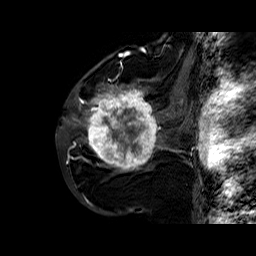
Breast MRI (dynamic contrast-enhanced), one sagittal slice; position 34 of 60 along the scan axis; dynamic contrast-enhanced series, time point 2 of 6 at this slice position (early post-contrast); 1.5 T; TE 6.4 ms, TR 32.8 ms; 256 × 256 image matrix, field of view 200 × 200 mm. Female patient. From the clinical record (not read from this slice): setting: breast cancer imaged before/during neoadjuvant chemotherapy; receptor status: HR-positive, HER2-negative.
Annotated regions visible in this slice (semi-automatically segmented with operator editing):
- analysis volume of interest (the breast-tissue region the enhancement analysis was run in; not a lesion): bounding box (x1, y1, x2, y2) in pixels: (86, 77, 163, 176)
- tumour enhancement mask (voxels above the 100 % enhancement threshold inside the analysis volume of interest): (86, 84, 160, 171)